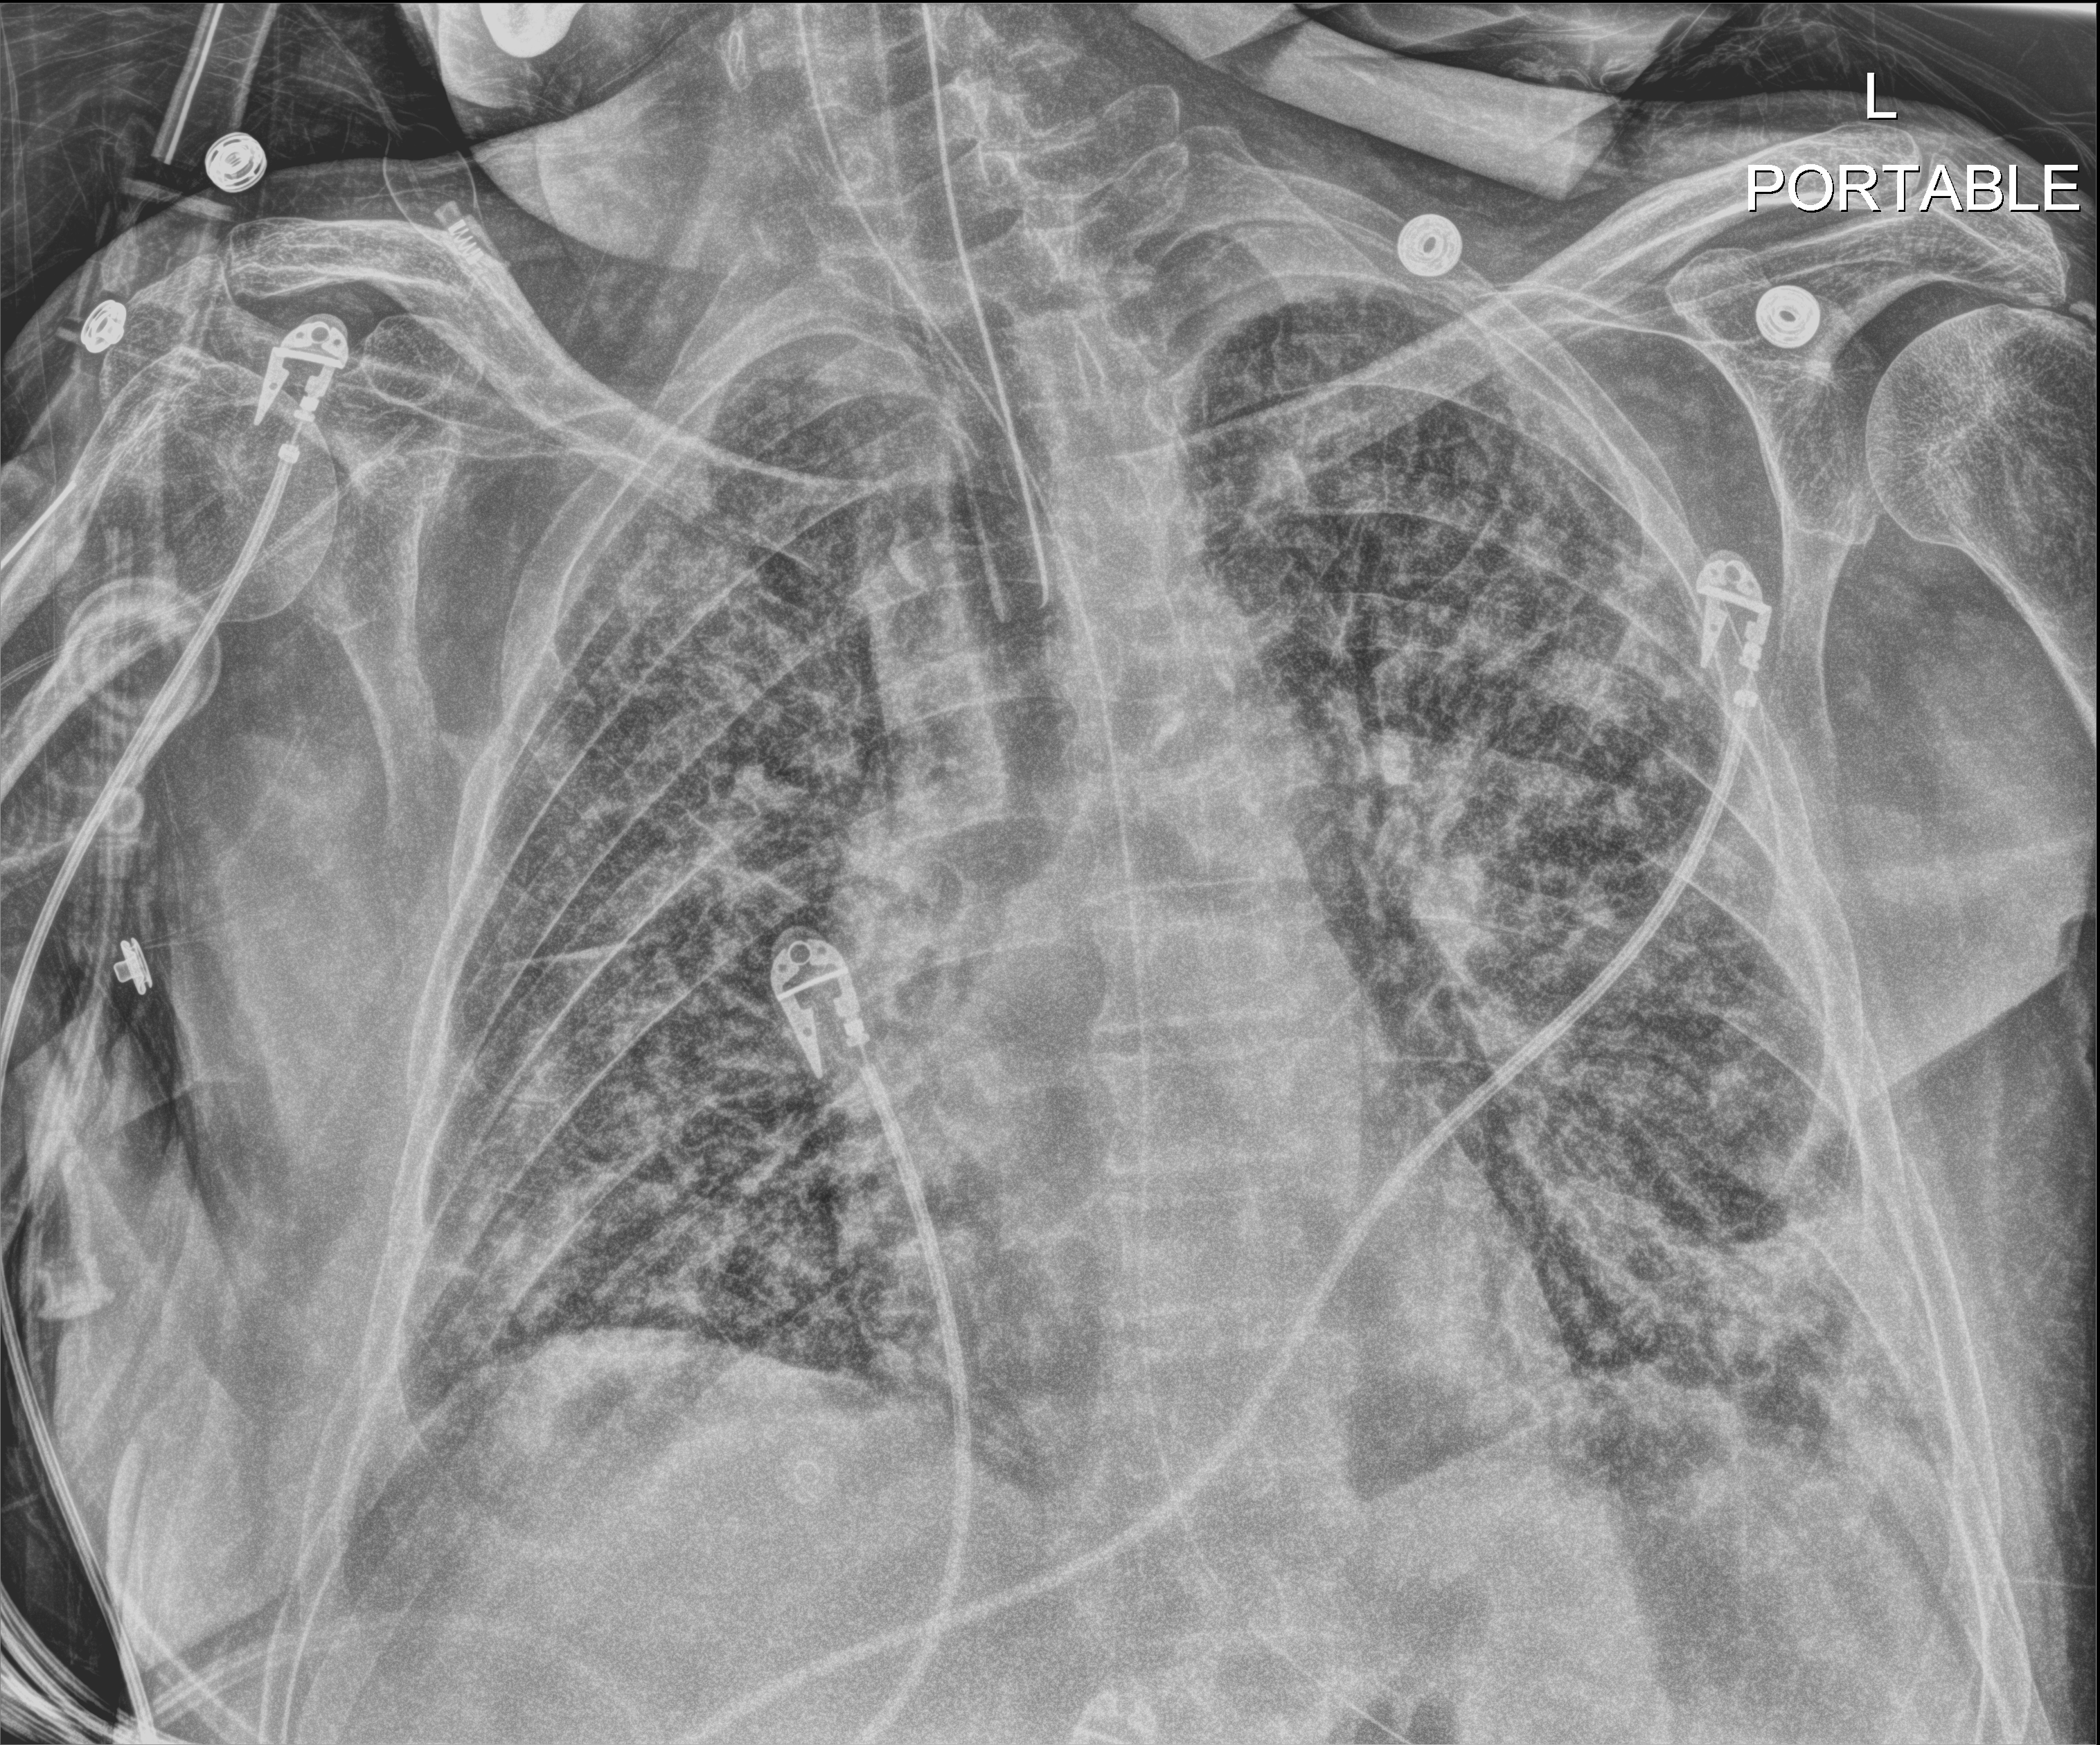
Chest X-ray; anteroposterior (AP) projection. Male patient hospitalised with COVID-19, age 60–74 years.
From the hospital-stay record, not from the radiograph (when in the stay this image was taken is not recorded): mechanically ventilated during this hospital stay: yes.